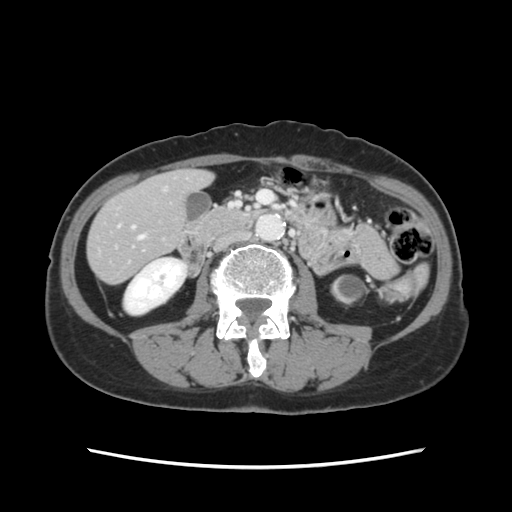
Contrast-enhanced abdominal CT, one axial slice; slice 27 of 120 in the series (ordered by position); intravenous contrast given; soft-tissue window (W 400 / L 40 HU); 2.5 mm slice thickness; 512 × 512 image matrix, field of view 330 × 330 mm. Female patient, age 70 years. From the clinical record (not read from this slice): diagnosis: colorectal cancer liver metastases, imaged before liver resection; multiple liver metastases: no; largest metastasis: 2.5 cm; disease in both lobes: no.
Outlined on this slice (outlined manually by an expert reader):
- hepatic veins: bounding box <139,236,145,239> (left, top, right, bottom; pixels)
- liver: <89,171,209,282>
- planned liver remnant (the part of the liver to remain after resection): <89,171,209,282>
- portal vein (with intrahepatic branches): <132,226,135,229>